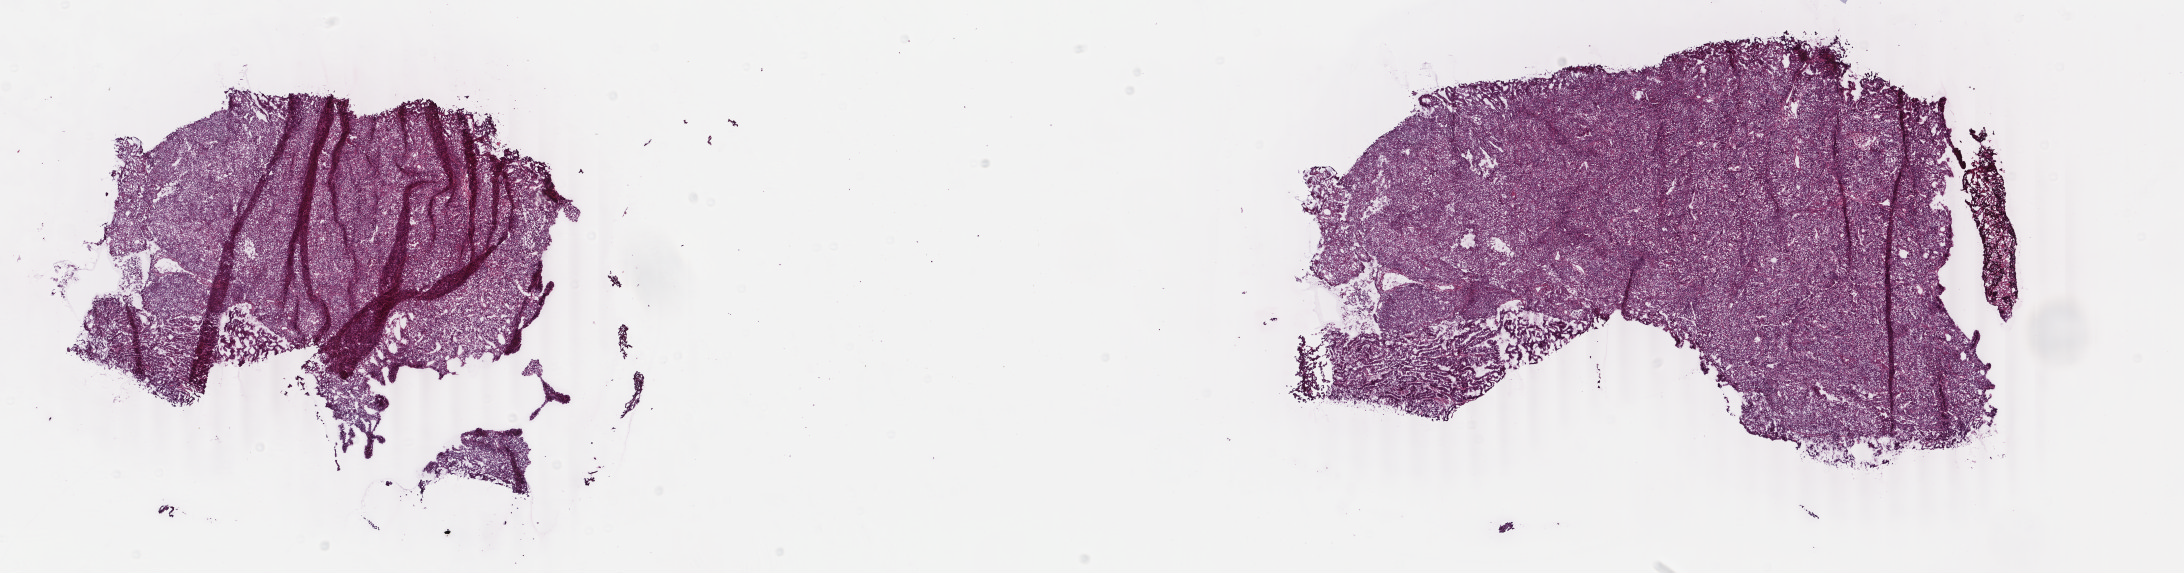
H&E whole-slide image — shown as a low-resolution overview of the whole scanned area (about 17.4 x 4.6 mm, from a 40x scan). Frozen section. Uterus, primary tumour sample. Female patient; age at initial diagnosis 63 years. Slide review estimates, as recorded: tumour cells 85%, tumour nuclei 92%.
Pathologic diagnosis: Endometrioid adenocarcinoma, NOS (endometrium).